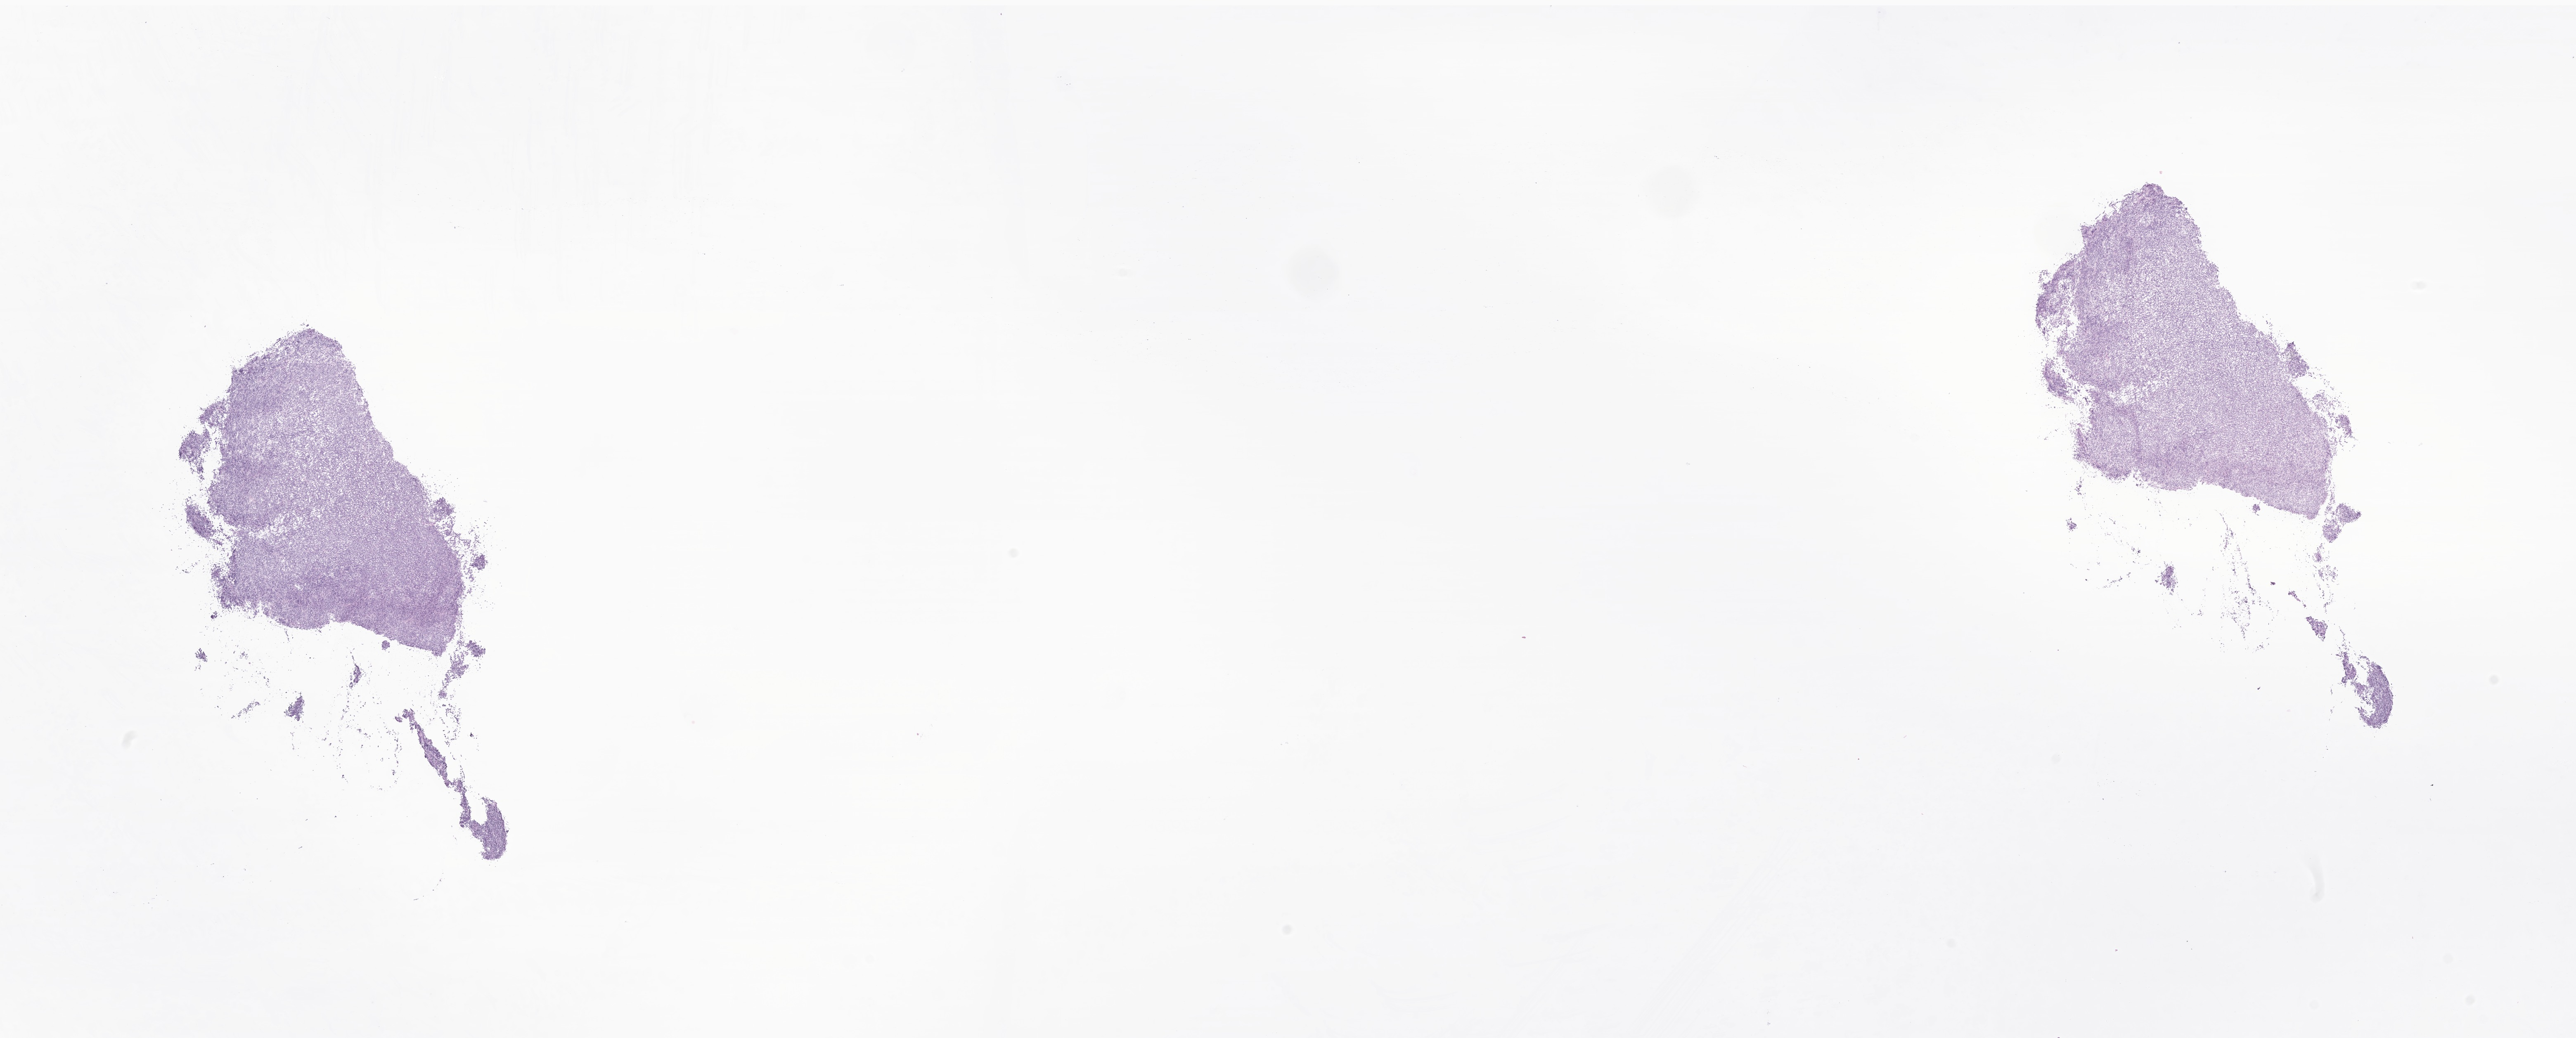
Haematoxylin and eosin whole-slide image of tumor tissue from the cerebellum, shown as a low-resolution overview of the whole scanned area (about 26.3 x 10.6 mm); frozen section (OCT-embedded). Patient: male, age 178 months.
Recorded diagnosis: Desmoplastic nodular medulloblastoma.